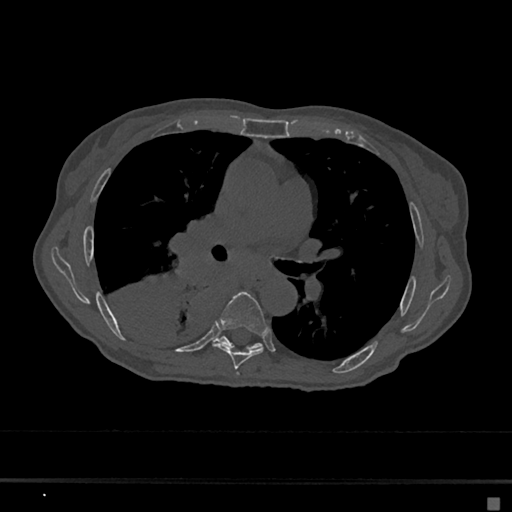
CT including the spine, one axial slice. Position 403 of 797 along the scan axis. Bone window (W 1800 / L 400 HU). 512 × 512 image matrix, field of view 360 × 360 mm. Female patient, age 68 years. Case-level facts recorded for this patient, not image findings: primary cancer: renal.
Structures marked on this image (semi-automatic segmentation, software-assisted and operator-edited):
- T6 vertebra: bounding box (x1, y1, x2, y2) in pixels: (213, 291, 268, 369)
- T7 vertebra: (216, 336, 262, 349)